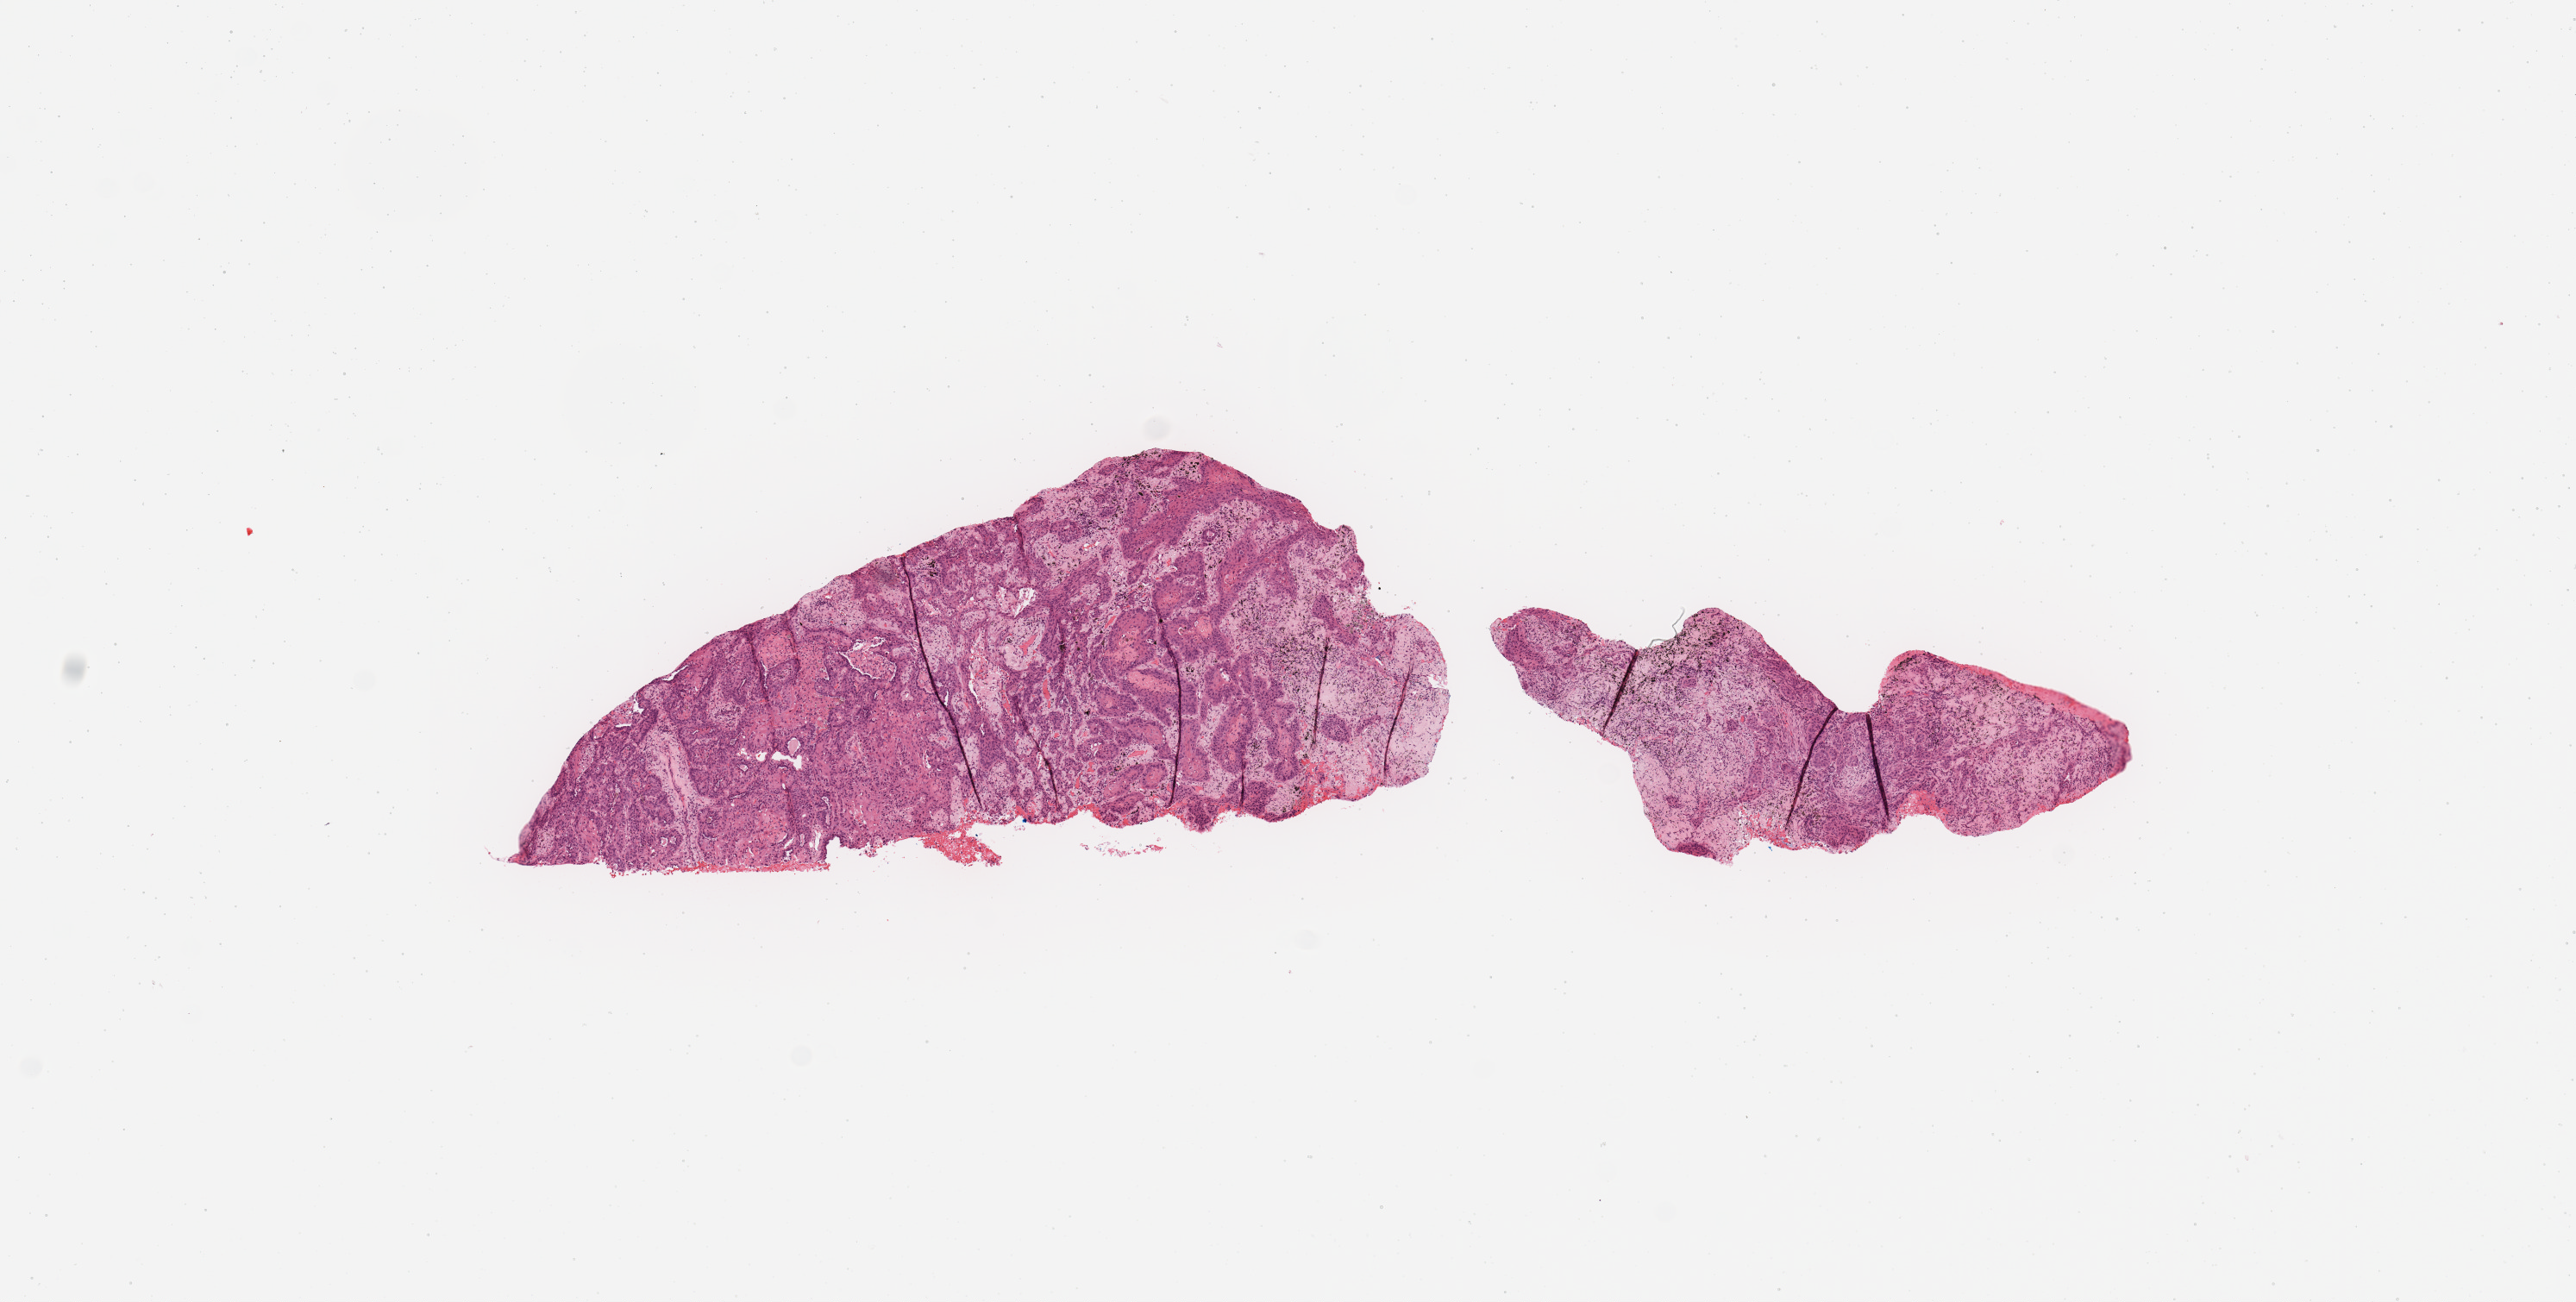
Digitized H&E tissue section (whole slide) — shown as a low-resolution overview of the whole scanned area (about 11.8 x 6.0 mm), tumour tissue sample, sampled site: lung. 70-year-old male patient. Histologic grade: G2 (moderately differentiated). Slide review estimates, as recorded: tumour nuclei 55%, necrosis 5%.
• histologic diagnosis: Squamous cell carcinoma, NOS
• primary tumour site (as recorded): right upper lobe
• AJCC pathologic stage: IB